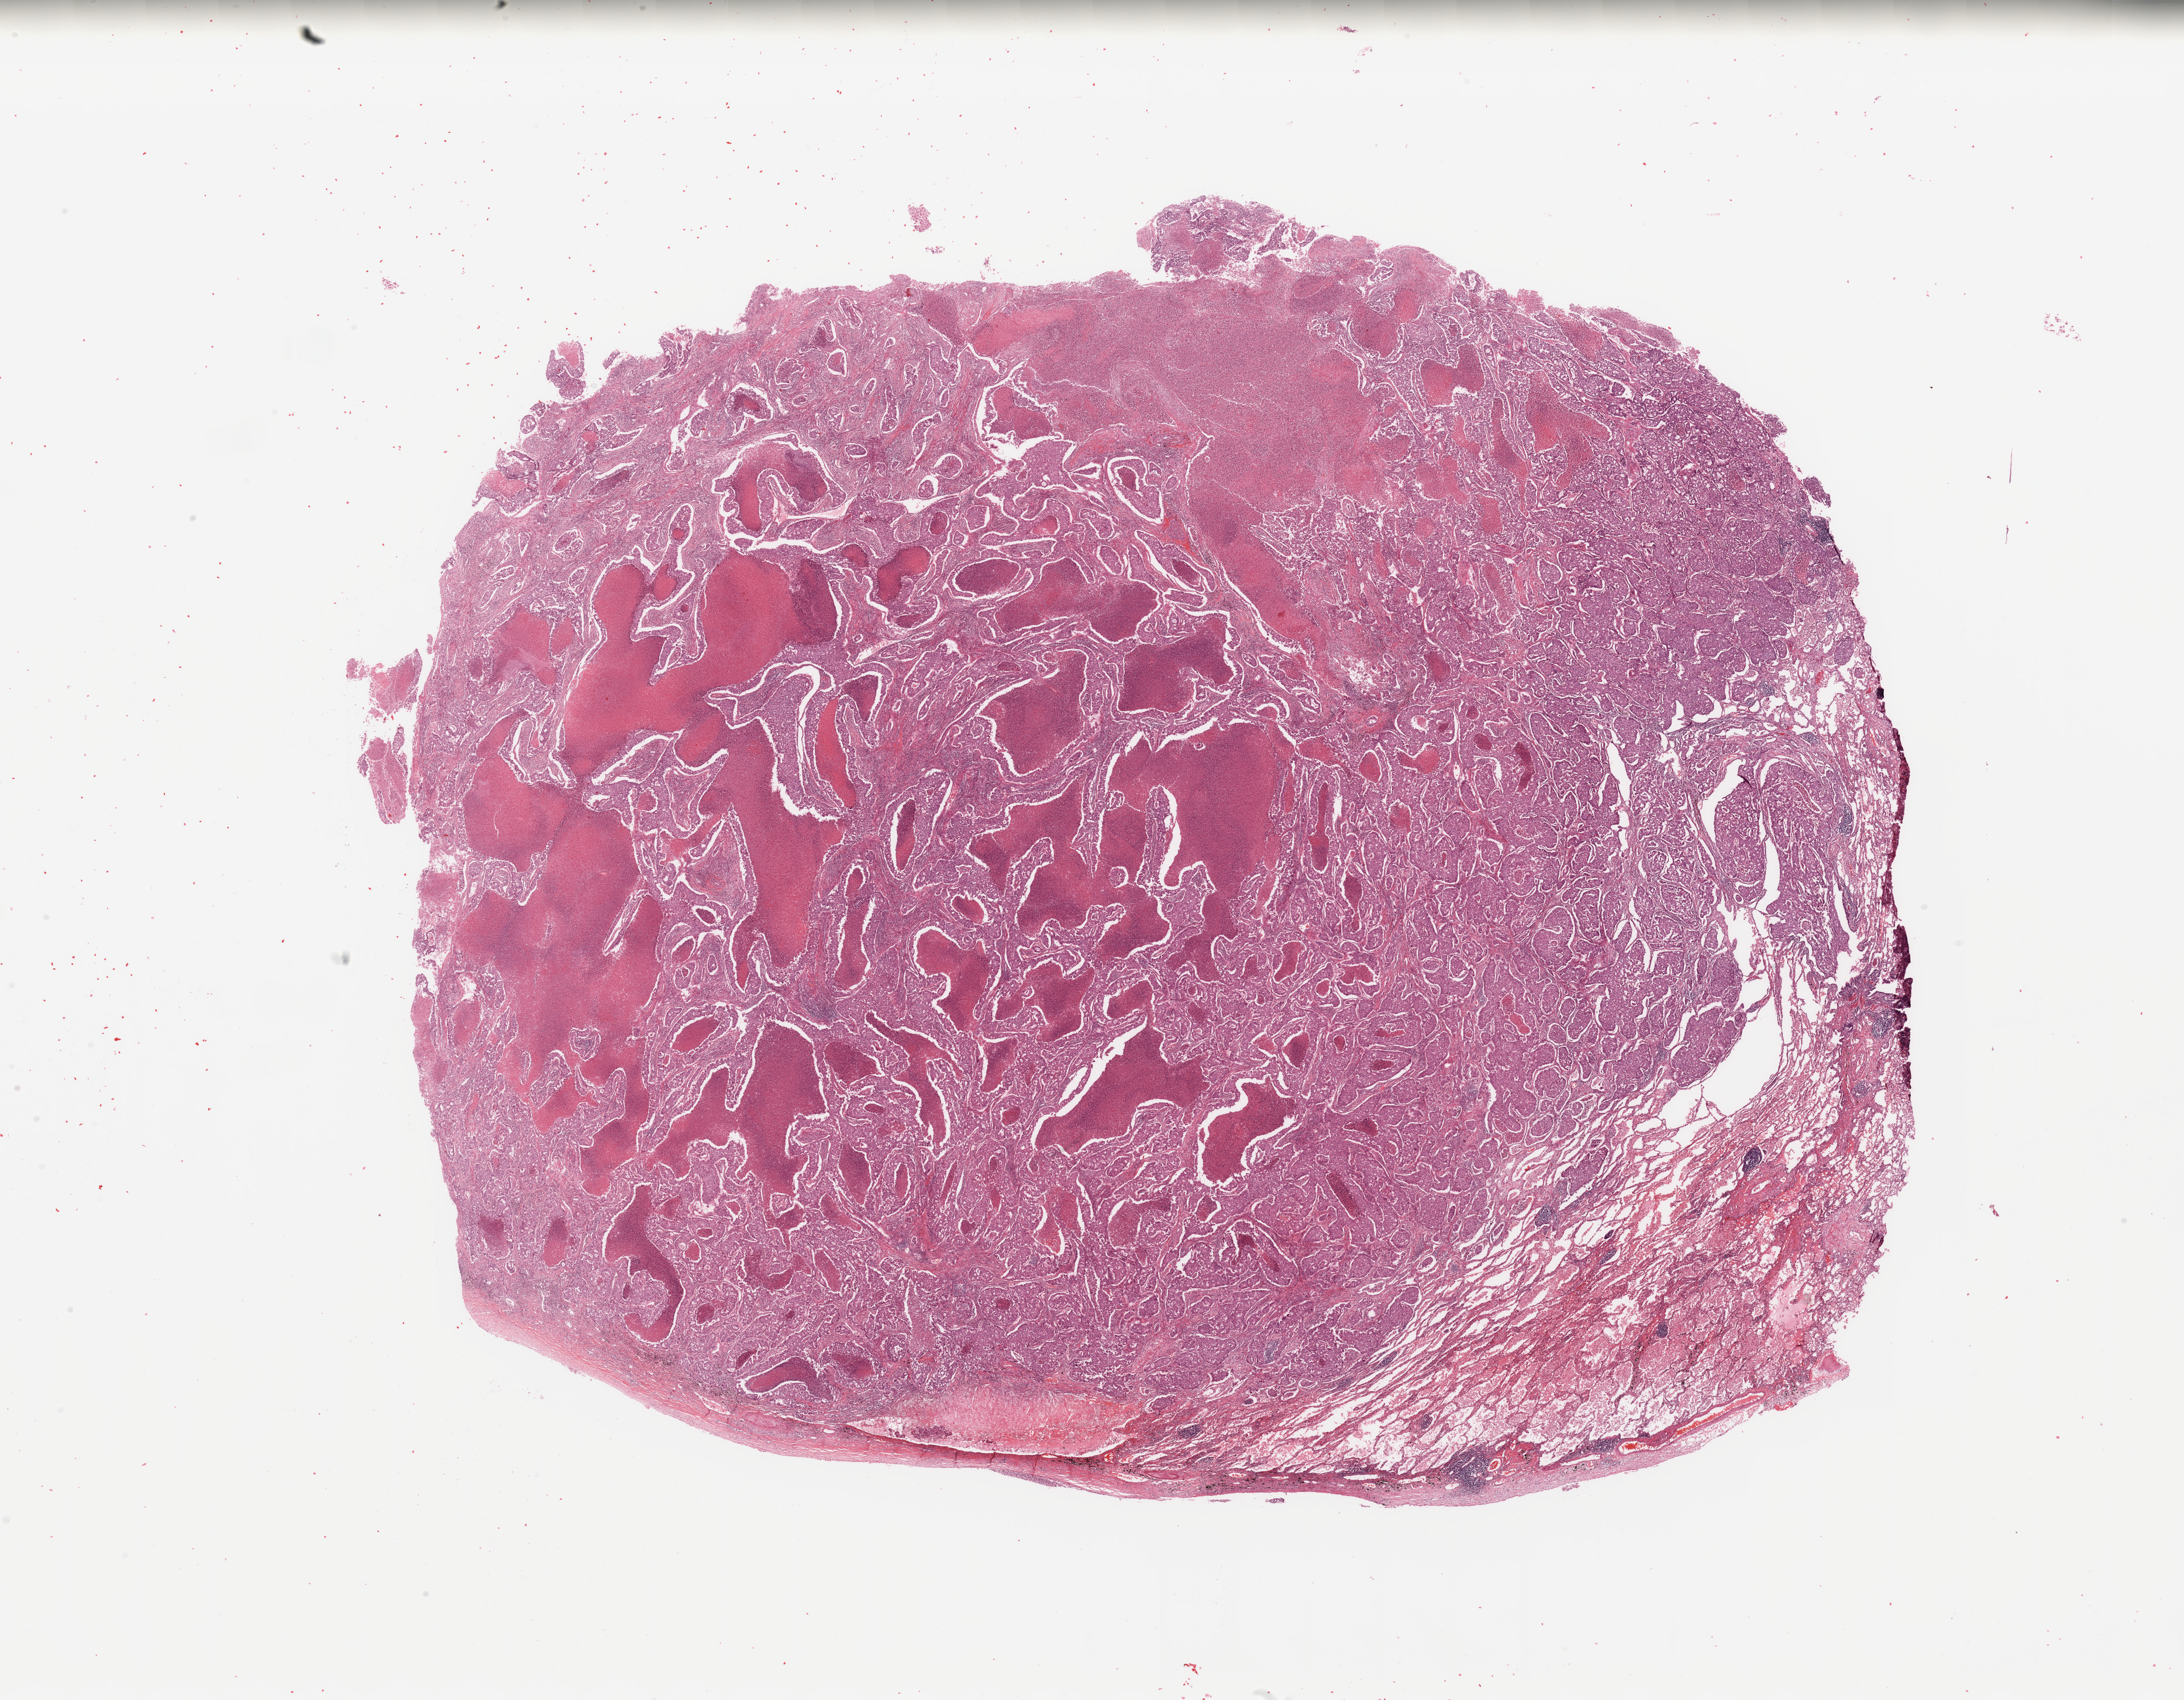
H&E whole-slide image — whole scanned area (about 29.5 x 23.0 mm, acquisition: 20x scan) shown as a low-resolution overview; tumour tissue sample, lung. 45-year-old male patient. Histologic grade: G3 (poorly differentiated).
• AJCC pathologic stage: IIB
• diagnosis: Adenocarcinoma, NOS